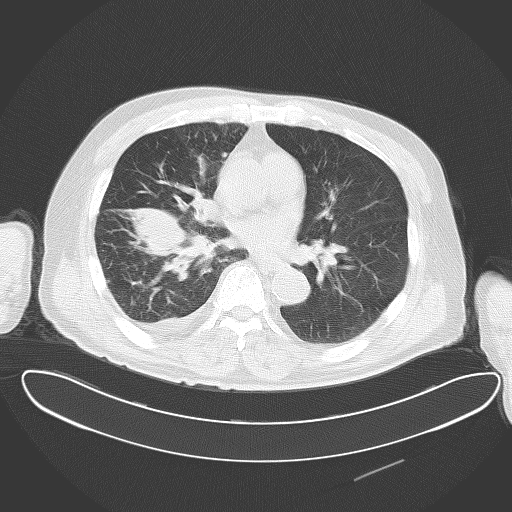
Chest CT, one axial slice. Reconstruction kernel B70f. 120 kVp. Lung window (W 1500 / L -600 HU). 5 mm slice thickness. 512 × 512 image matrix, field of view 427 × 427 mm. Patient: male, 78 years. Case-level facts recorded for this patient, not image findings: clinical TNM (as recorded): T2 N1 M1.
Outlined on this slice (rectangle marked by the reading radiologist):
- lung tumour (recorded histology: adenocarcinoma): box from (x=127, y=200) to (x=216, y=281) px